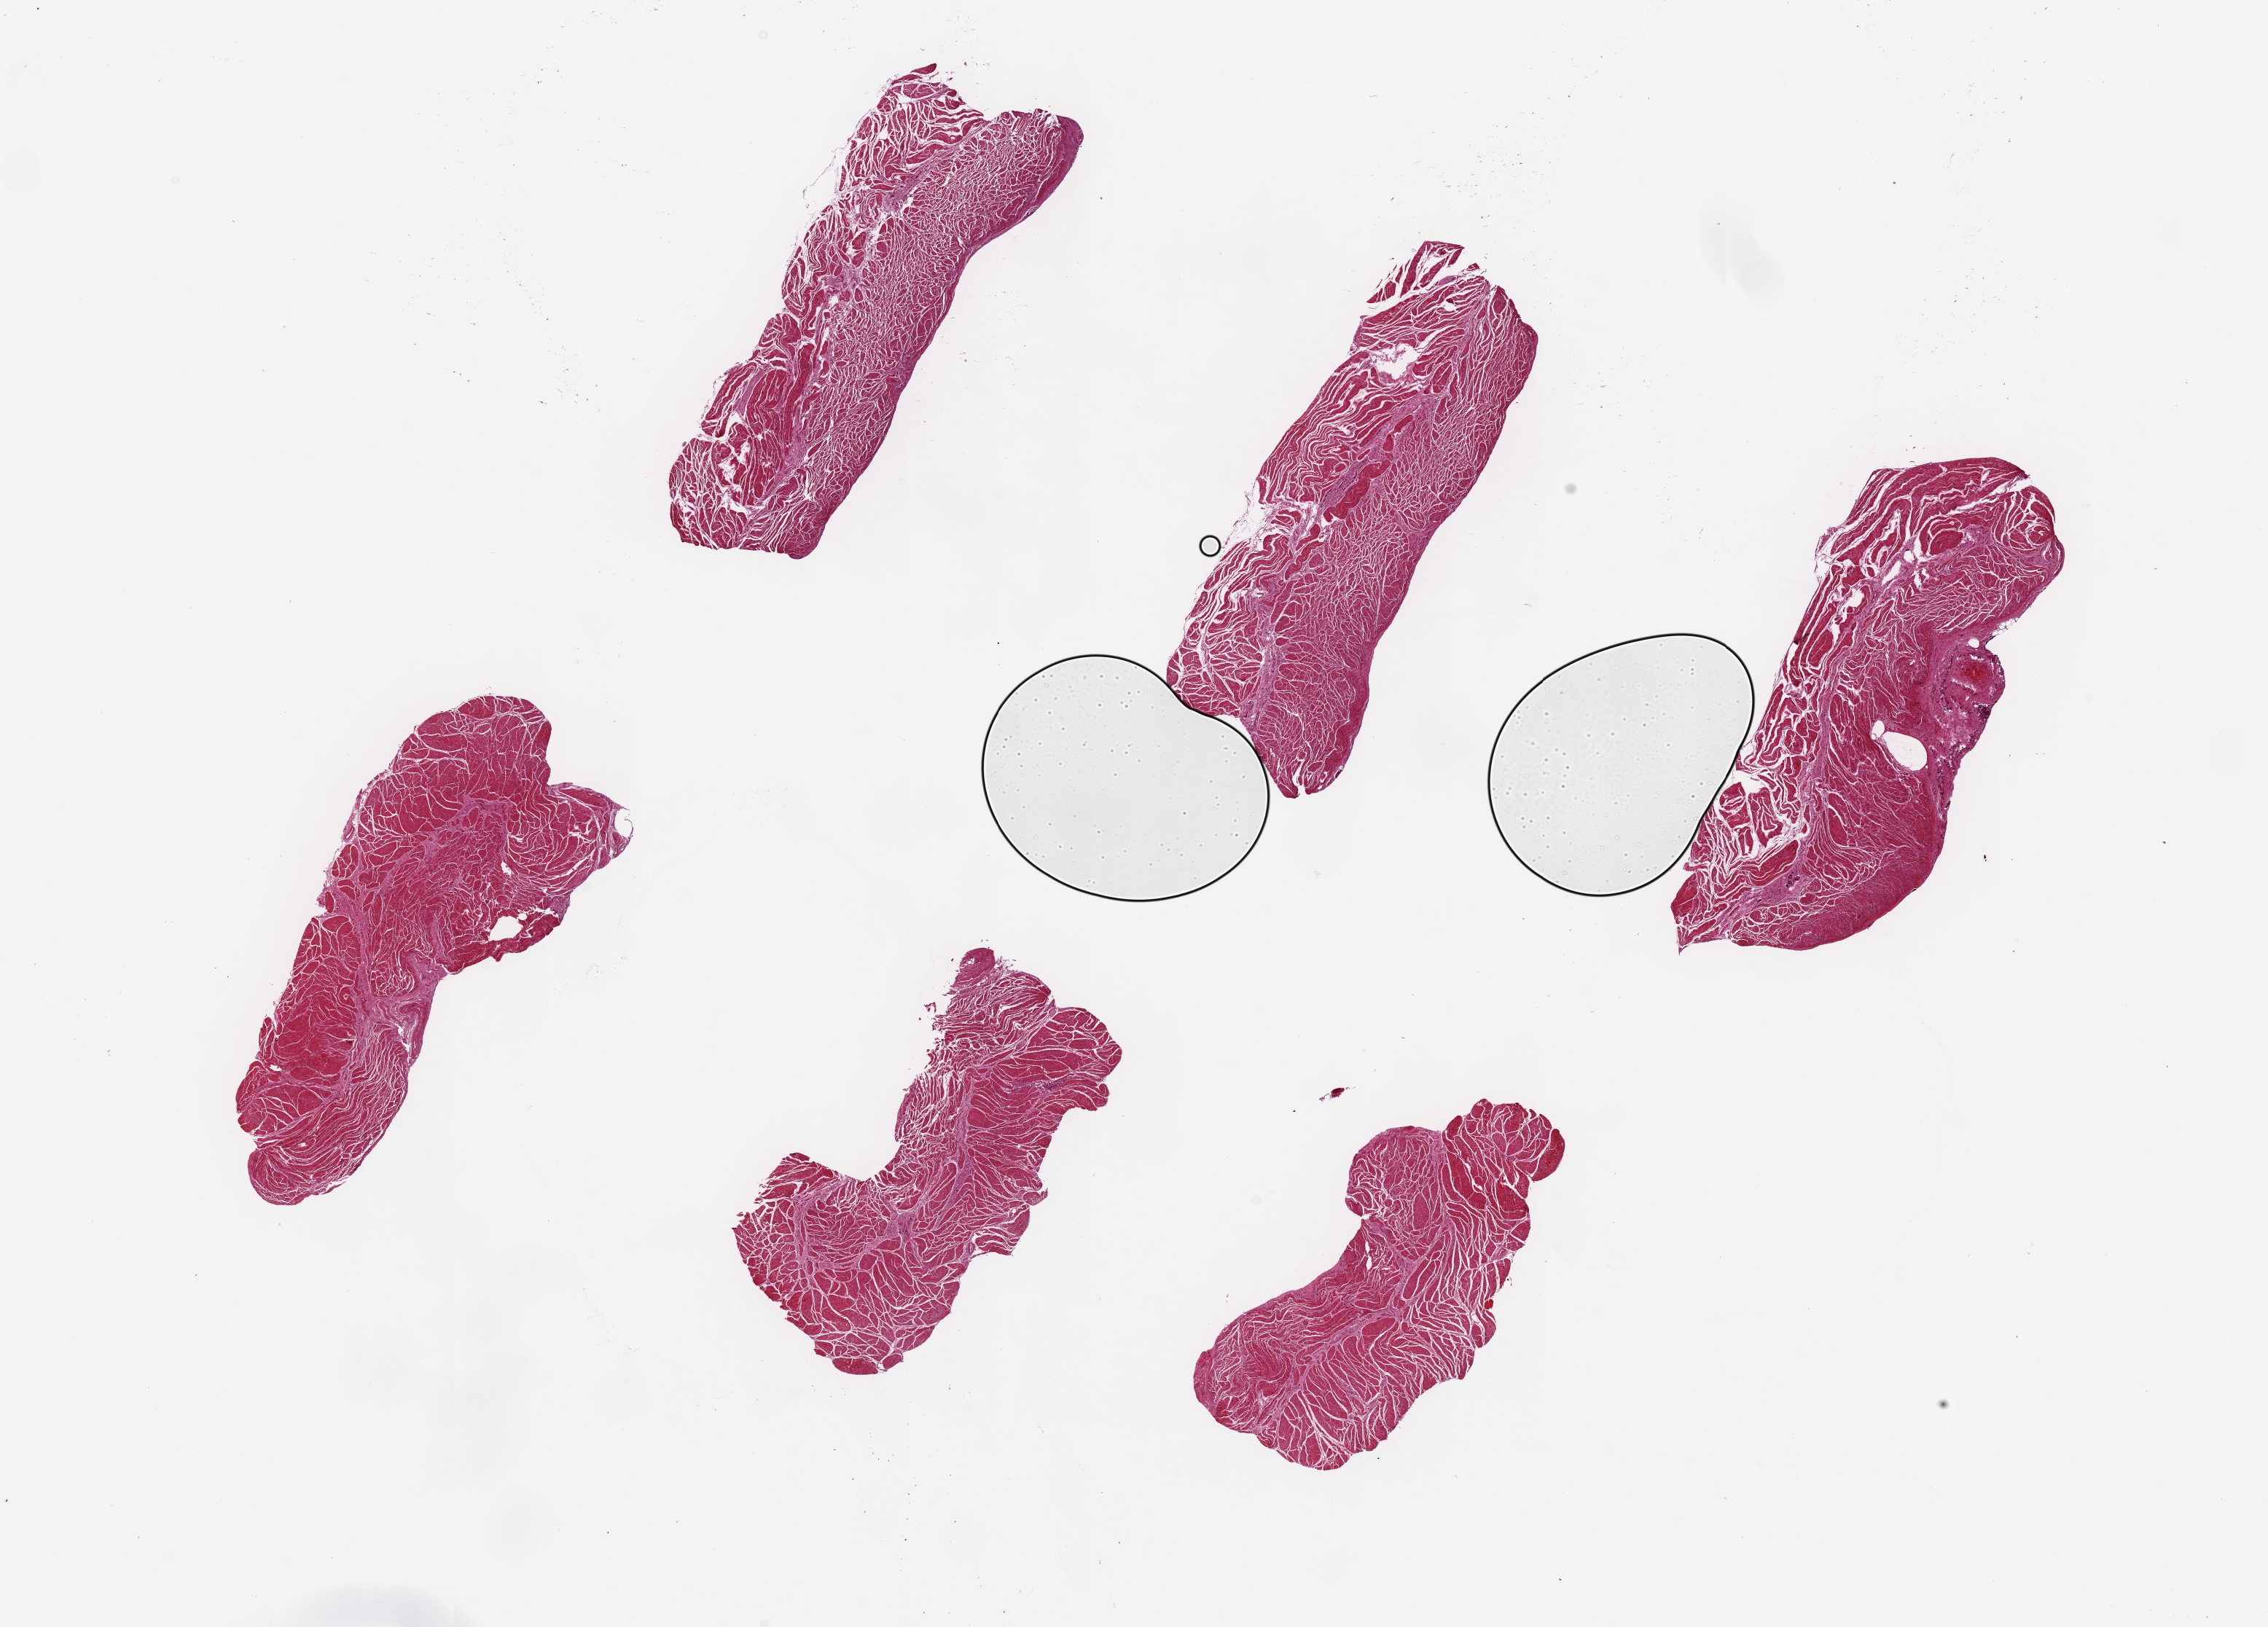
Whole-slide image, haematoxylin and eosin stain — shown as a low-resolution overview of the whole scanned area (about 24.6 x 17.7 mm, slide scanned at 20x). PAXgene-fixed paraffin-embedded (PFPE) section. Sampled site (target tissue): esophageal muscle. Donor tissue sample. Donor sex: male.
Review note (as recorded): 6 pieces, up to 6x2mm.